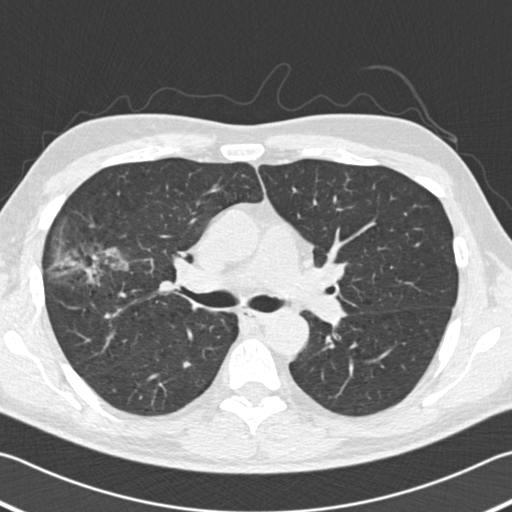
Chest CT (low-dose screening protocol), one axial image. Second screening round (one year after baseline). Lung window (W 1500 / L -600 HU). 2 mm slice thickness. Male, age 56 years at enrolment. Former smoker at enrolment.
Expert-annotated lung lesion, bounding box (x1, y1, x2, y2) in pixels: (47, 233, 130, 298). Reader record for this screening exam (exam-level; its link to the box is not recorded): non-calcified nodule or mass ≥4 mm, right upper lobe, 18 × 14 mm, spiculated (stellate) margins, soft tissue attenuation, pre-existing on the prior screen: yes; interval growth: yes. Participant outcome: lung cancer diagnosed 42 days after this screen — bronchiolo-alveolar adenocarcinoma, NOS, right upper lobe, well differentiated (G1), stage IIB (AJCC 6th edition), 30 mm at pathology.